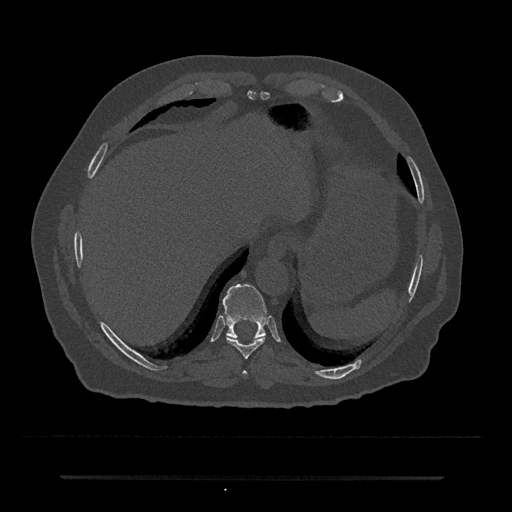
CT including the spine, one axial slice; 120 kVp; bone window (W 1800 / L 400 HU); 512 × 512 image matrix, field of view 437 × 437 mm. Patient: male, 69 years. From the clinical record (not read from this slice): primary cancer: prostate.
Structures marked on this image (semi-automatic segmentation, software-assisted and operator-edited):
- T10 vertebra: bounding box (x1, y1, x2, y2) in pixels: (222, 284, 267, 339)
- T8 vertebra: (243, 371, 248, 376)
- T9 vertebra: (226, 336, 266, 359)